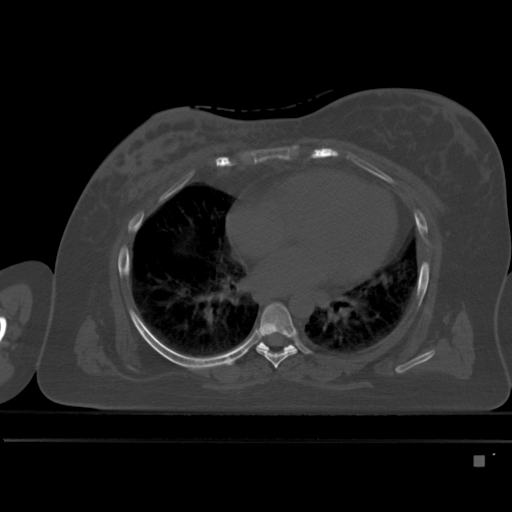
CT including the spine, one axial slice. Position 301 of 495 along the scan axis. Bone window (W 1800 / L 400 HU). 1.5 mm slice thickness. 512 × 512 image matrix, field of view 404 × 404 mm. Female patient, age 33 years. Case-level facts recorded for this patient, not image findings: primary cancer: breast.
Structures marked on this image (semi-automatically segmented with operator editing):
- T6 vertebra: bounding box [x1, y1, x2, y2] px = [256, 302, 297, 368]
- T7 vertebra: [258, 341, 295, 350]